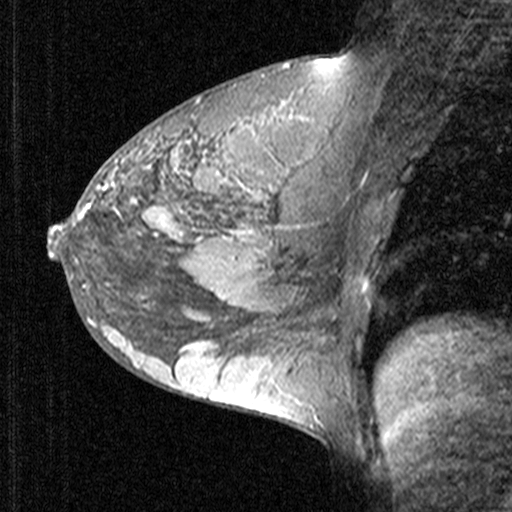
Breast MRI (dynamic contrast-enhanced), one sagittal slice. Position 25 of 44 along the scan axis. Dynamic contrast-enhanced study with each time point stored as its own series, time point 2 of 3 at this slice position (early post-contrast, ordered by acquisition time). 1.5 T. TE 4.5 ms, TR 11 ms. 3 mm slice thickness. 512 × 512 image matrix. Patient: female, 27 years. Case-level facts recorded for this patient, not image findings: setting: breast cancer imaged before/during neoadjuvant chemotherapy; receptor status: HR-positive, HER2-negative.
Outlined on this slice (semi-automatic segmentation, software-assisted and operator-edited):
- analysis volume of interest (the breast-tissue region the enhancement analysis was run in; not a lesion): box from (x=68, y=146) to (x=165, y=239) px
- tumour enhancement mask (voxels above the 90 % enhancement threshold inside the analysis volume of interest): (x=72, y=182)–(x=158, y=235)